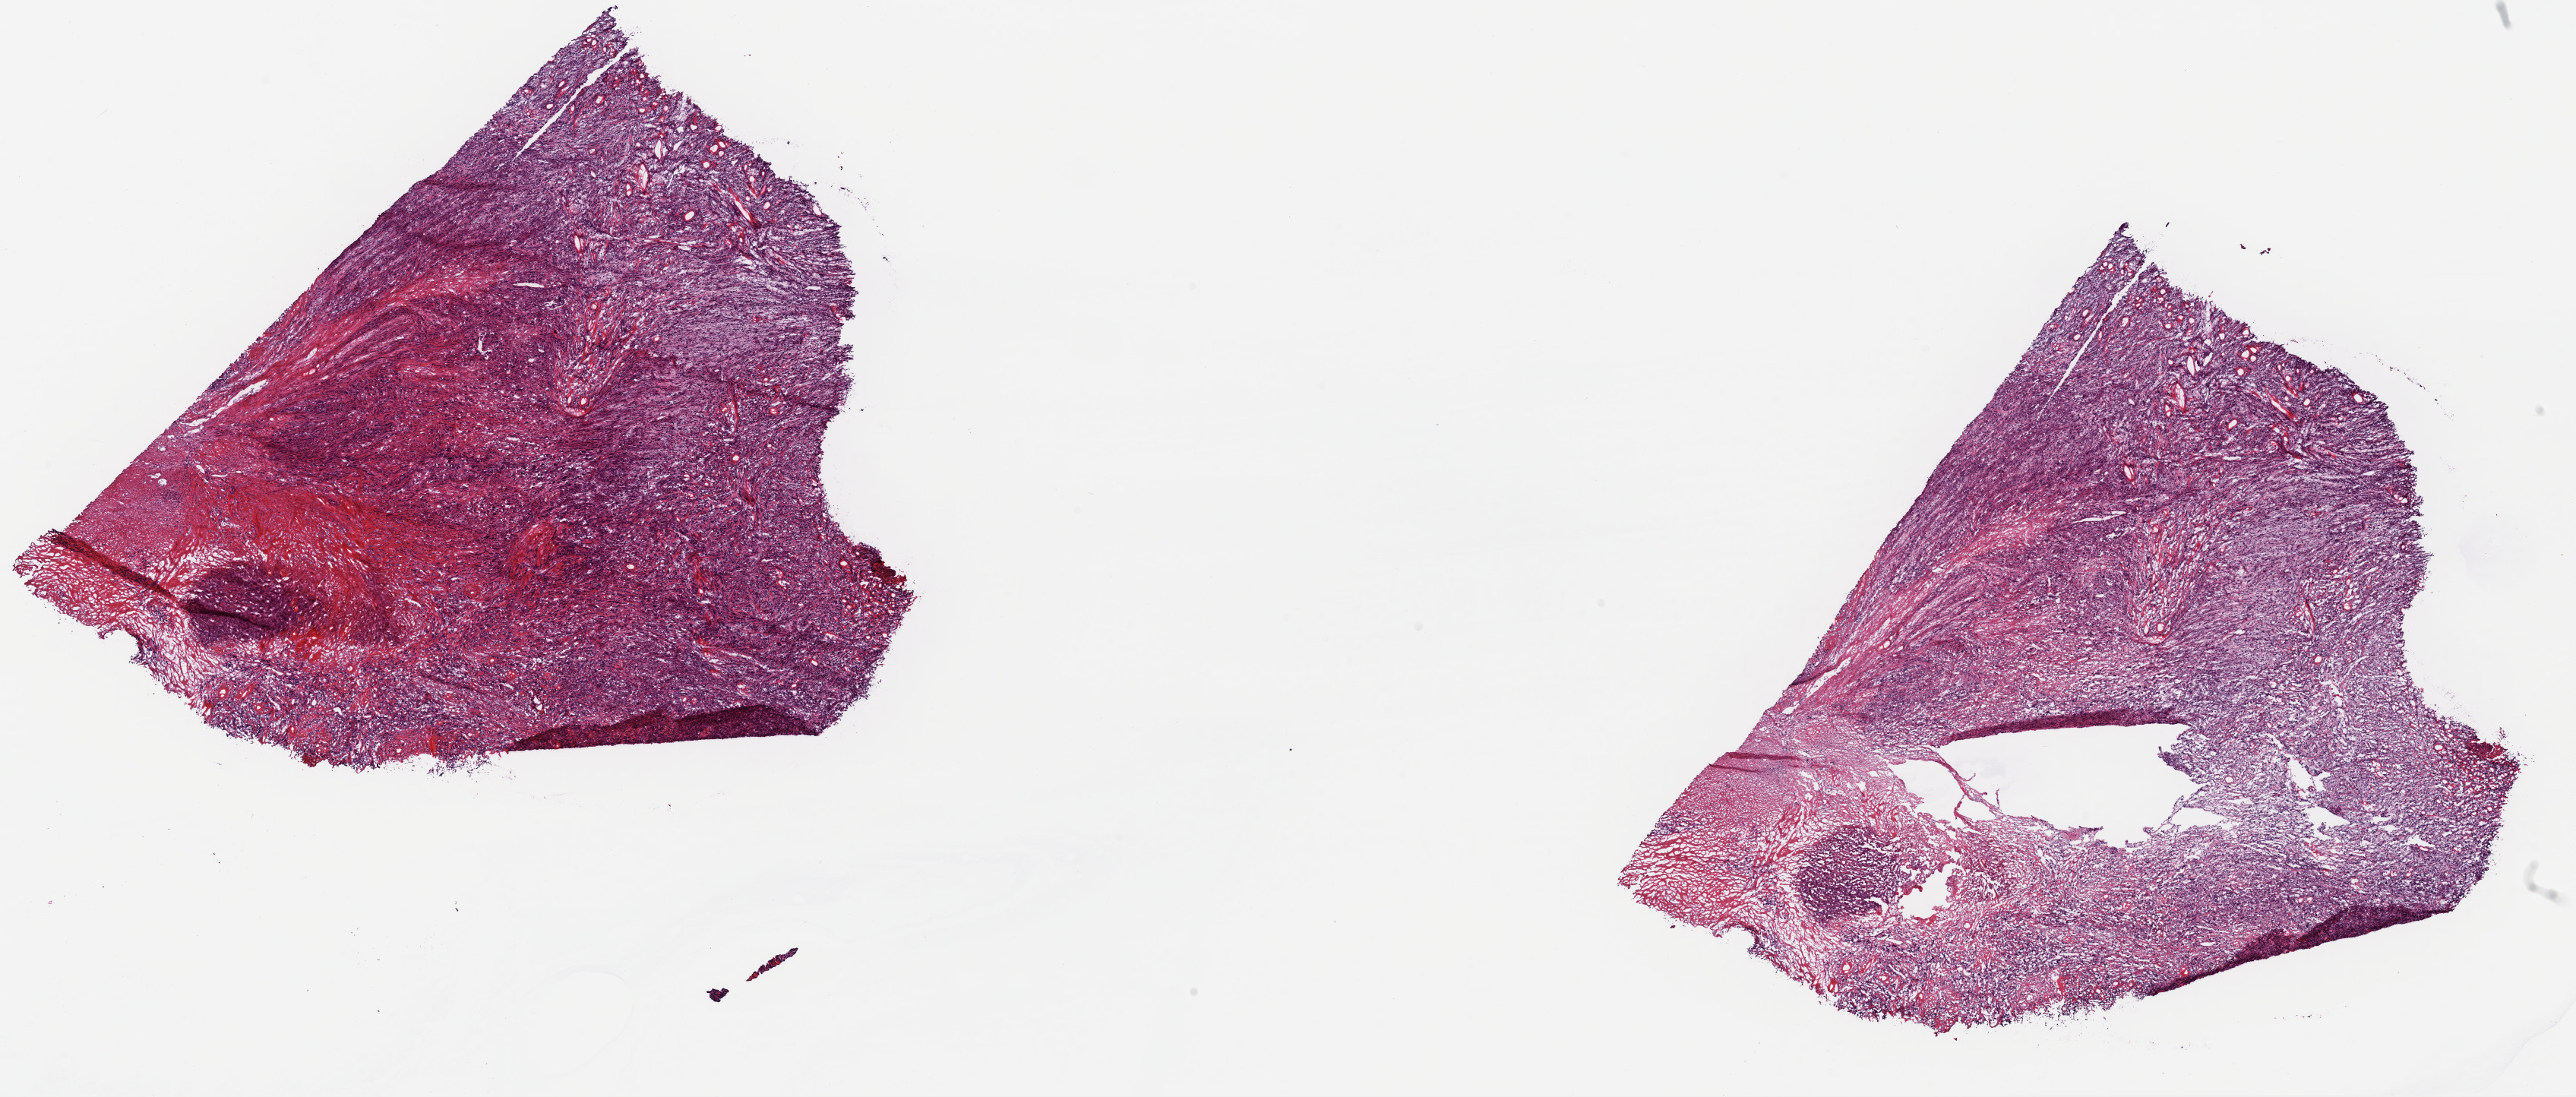
Digitized Hematoxylin and eosin (H&E) stained tissue section (whole slide), shown as a low-resolution overview of the whole scanned area (about 26.8 x 11.4 mm, slide scanned at 40x), frozen section, metastatic tumour sample. Patient: male, age at initial diagnosis 45 years. Pathologist review of this section (percent, as recorded): tumour cells 75%, tumour nuclei 75%, normal cells 0%, stromal cells 20%, necrosis 5%. Infiltration values recorded for this section: lymphocyte infiltration 2%, monocyte infiltration 1%, neutrophil infiltration 1%.
* this section: metastatic tumour tissue
* patient diagnosis: Malignant melanoma, NOS